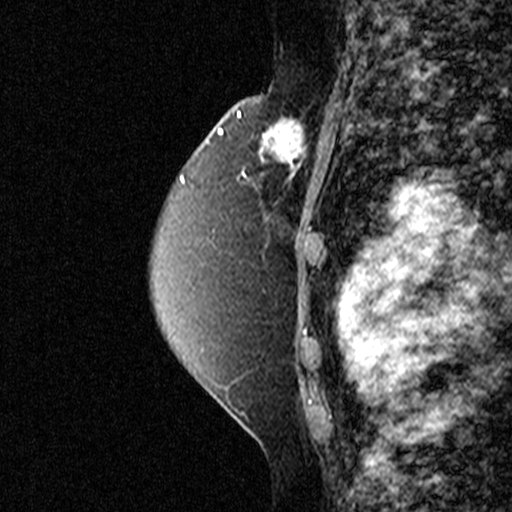
Breast MRI (dynamic contrast-enhanced), one sagittal slice; slice 30 of 44 in the series (ordered by position); dynamic contrast-enhanced study with each time point stored as its own series, time point 2 of 3 at this slice position (early post-contrast, ordered by acquisition time); 1.5 T; TE 4.5 ms, TR 11 ms; 3 mm slice thickness; 512 × 512 image matrix, field of view 200 × 200 mm. Female patient, age 49 years. From the clinical record (not read from this slice): setting: breast cancer imaged before/during neoadjuvant chemotherapy; receptor status: triple-negative.
Annotated regions visible in this slice (semi-automatically segmented with operator editing):
- analysis volume of interest (the breast-tissue region the enhancement analysis was run in; not a lesion): bounding box (x1, y1, x2, y2) in pixels: (246, 100, 335, 197)
- tumour enhancement mask (voxels above the 90 % enhancement threshold inside the analysis volume of interest): (259, 115, 308, 177)